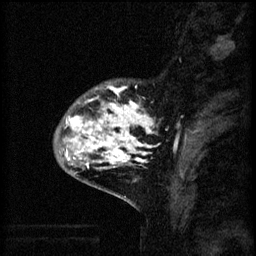
Breast MRI (dynamic contrast-enhanced), one sagittal slice; position 15 of 60 along the scan axis; 3 images stored at this slice position (order not interpretable as contrast timing); 1.5 T; TE 4.2 ms, TR 8.2 ms; 2 mm slice thickness; 256 × 256 image matrix. Patient: female, 41 years.
Annotated regions visible in this slice (semi-automatically segmented with operator editing):
- analysis volume of interest (the breast-tissue region the enhancement analysis was run in; not a lesion): box from (x=55, y=80) to (x=159, y=175) px
- tumour enhancement mask (voxels above the 70 % enhancement threshold inside the analysis volume of interest): (x=64, y=86)–(x=158, y=169)